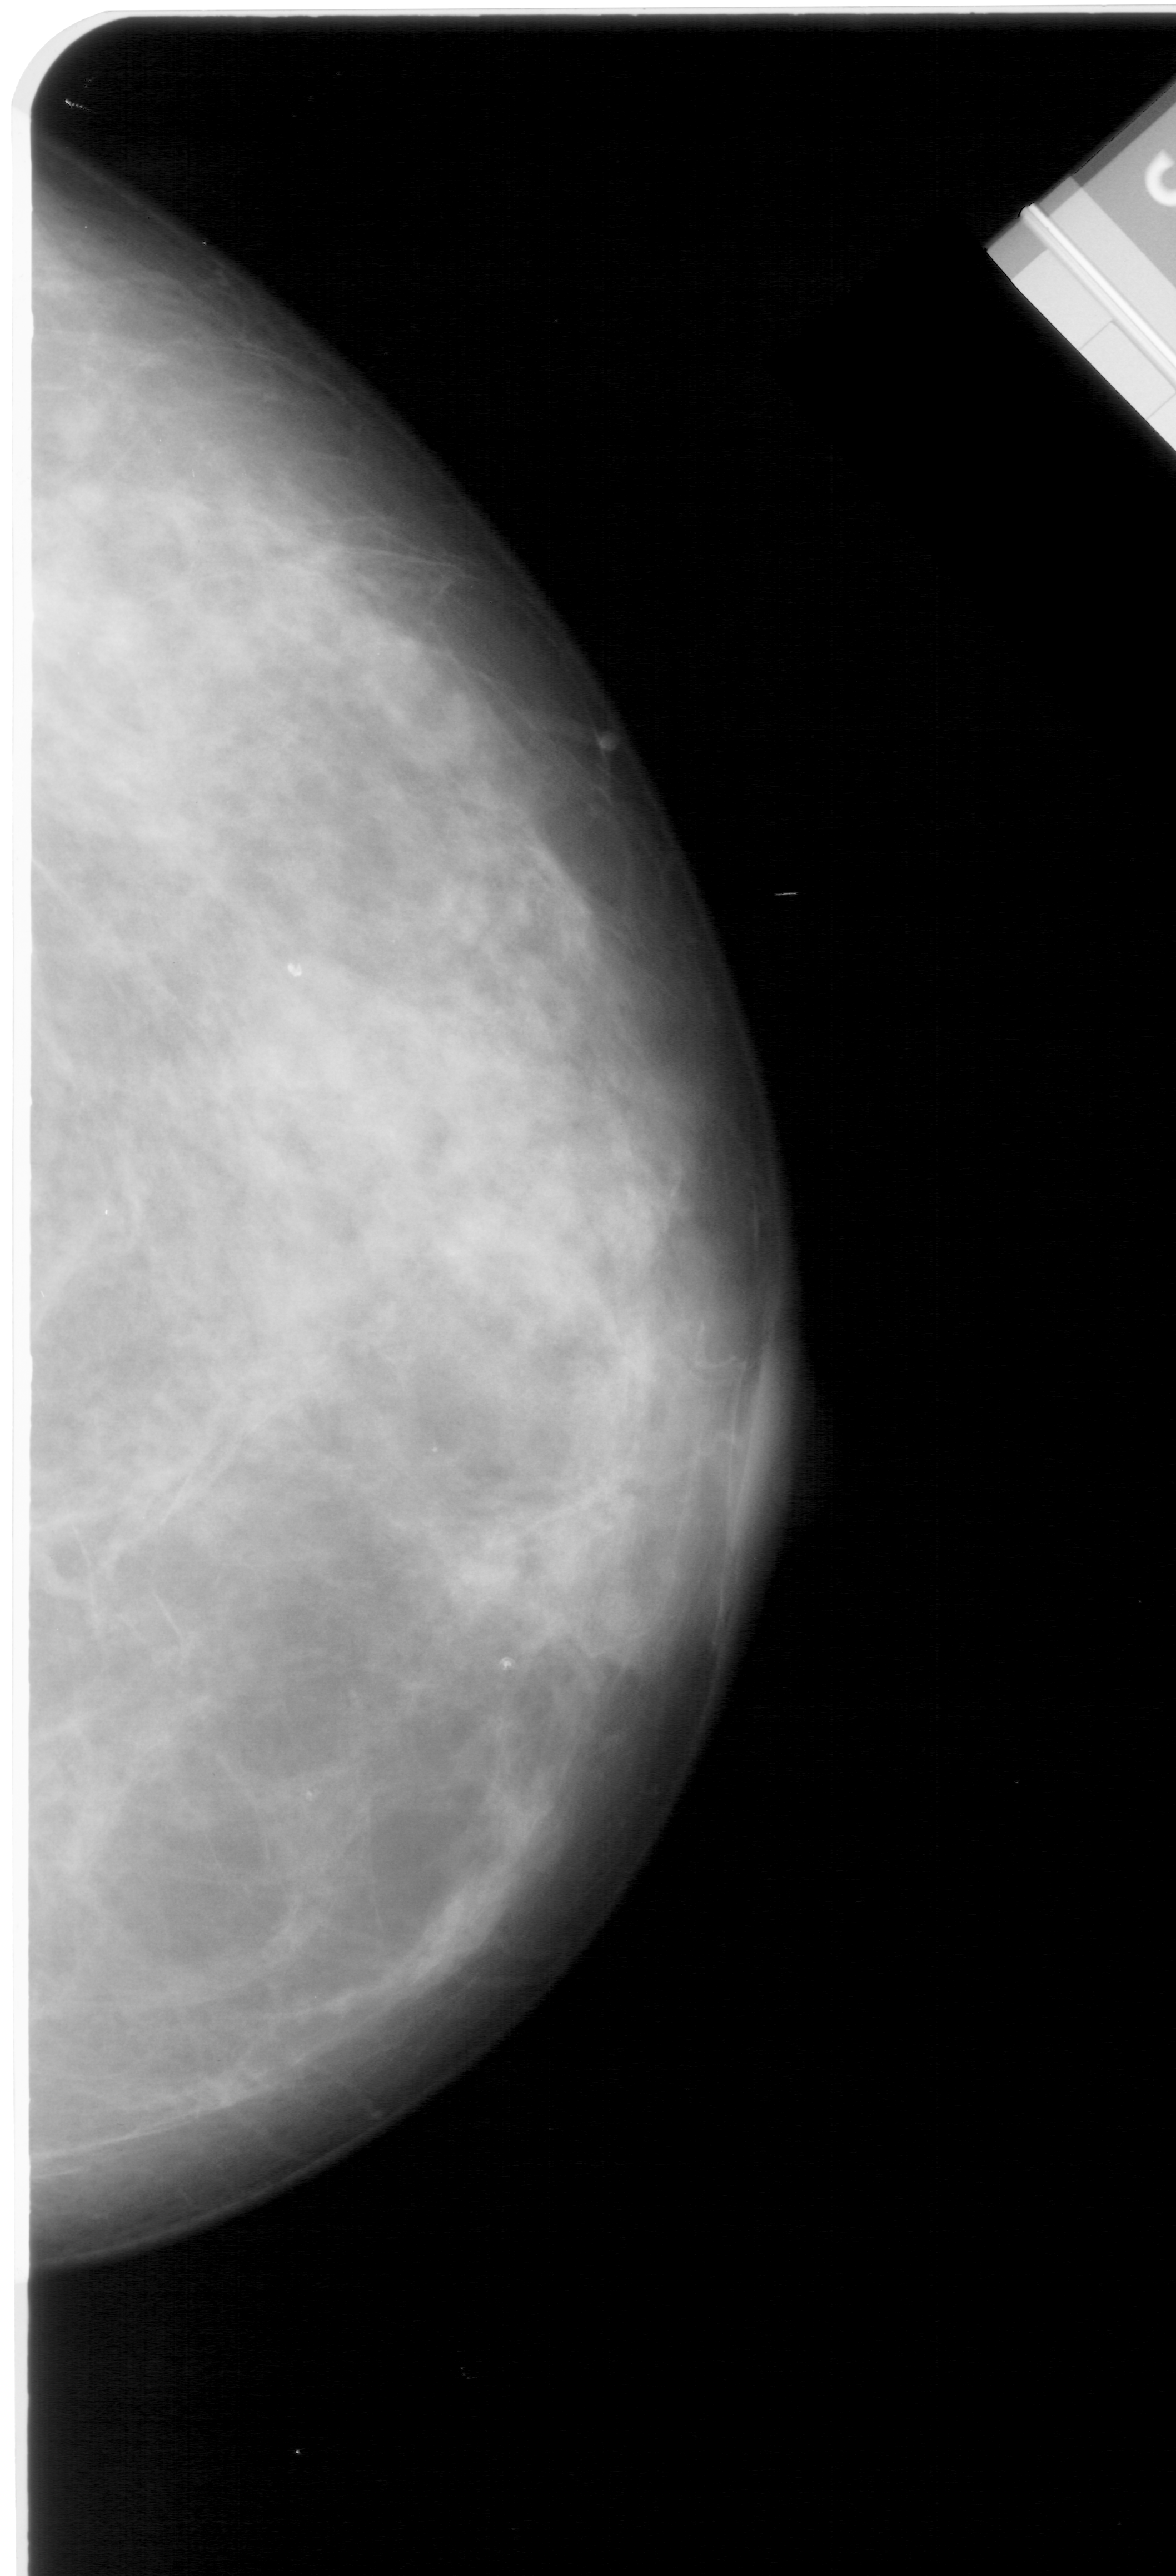
Scanned film-screen mammogram. Right breast. CC view. 1176 × 2576 image matrix.
Expert-marked regions of interest on this image (one box per marked abnormality):
- mass, shape irregular, margins ill defined; BI-RADS assessment category 4; subtlety rating 3 on a 1 (subtle) to 5 (obvious) scale; pathology (as recorded): benign: bounding box (x1, y1, x2, y2) in pixels: (23, 559, 161, 731)